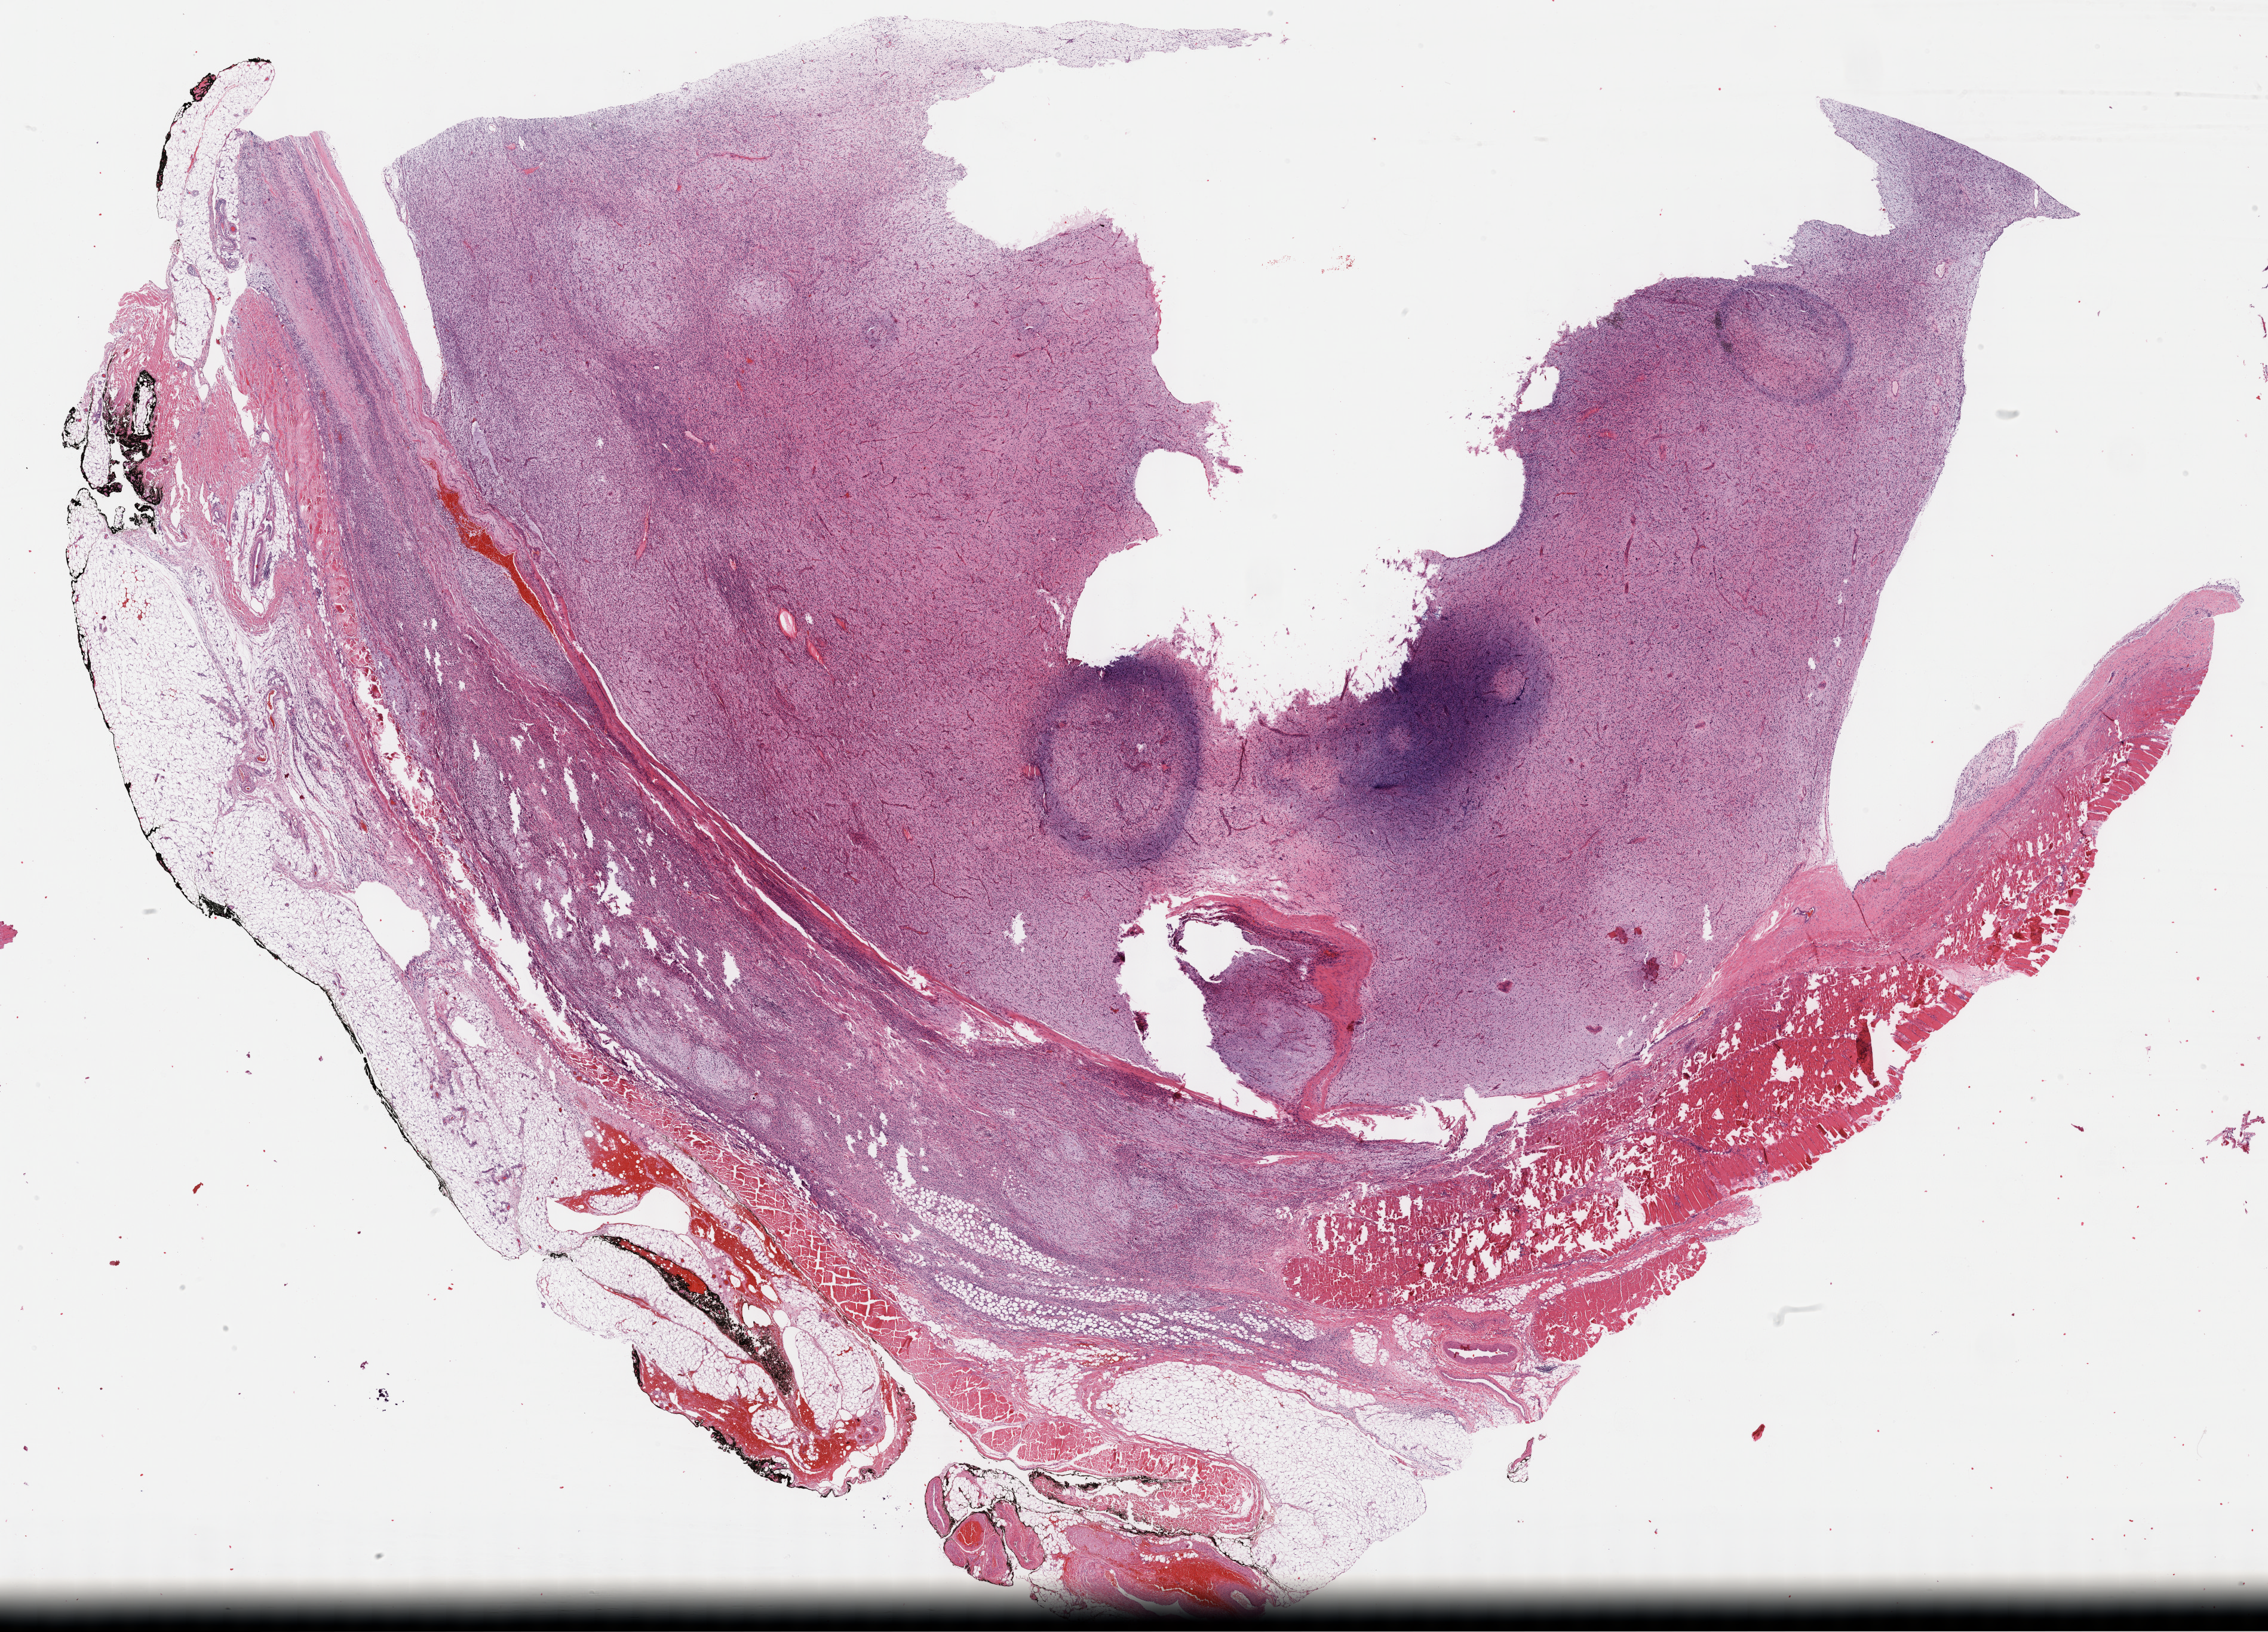
Whole-slide histology image, H&E, shown as a low-resolution overview of the whole scanned area (about 30.7 x 22.1 mm, from a 40x scan), formalin-fixed paraffin-embedded (FFPE) diagnostic section, primary tumour sample from the connective, subcutaneous and other soft tissues. Male, age 35 years at initial diagnosis.
• diagnosis: Fibromyxosarcoma (connective, subcutaneous and other soft tissues of lower limb and hip)